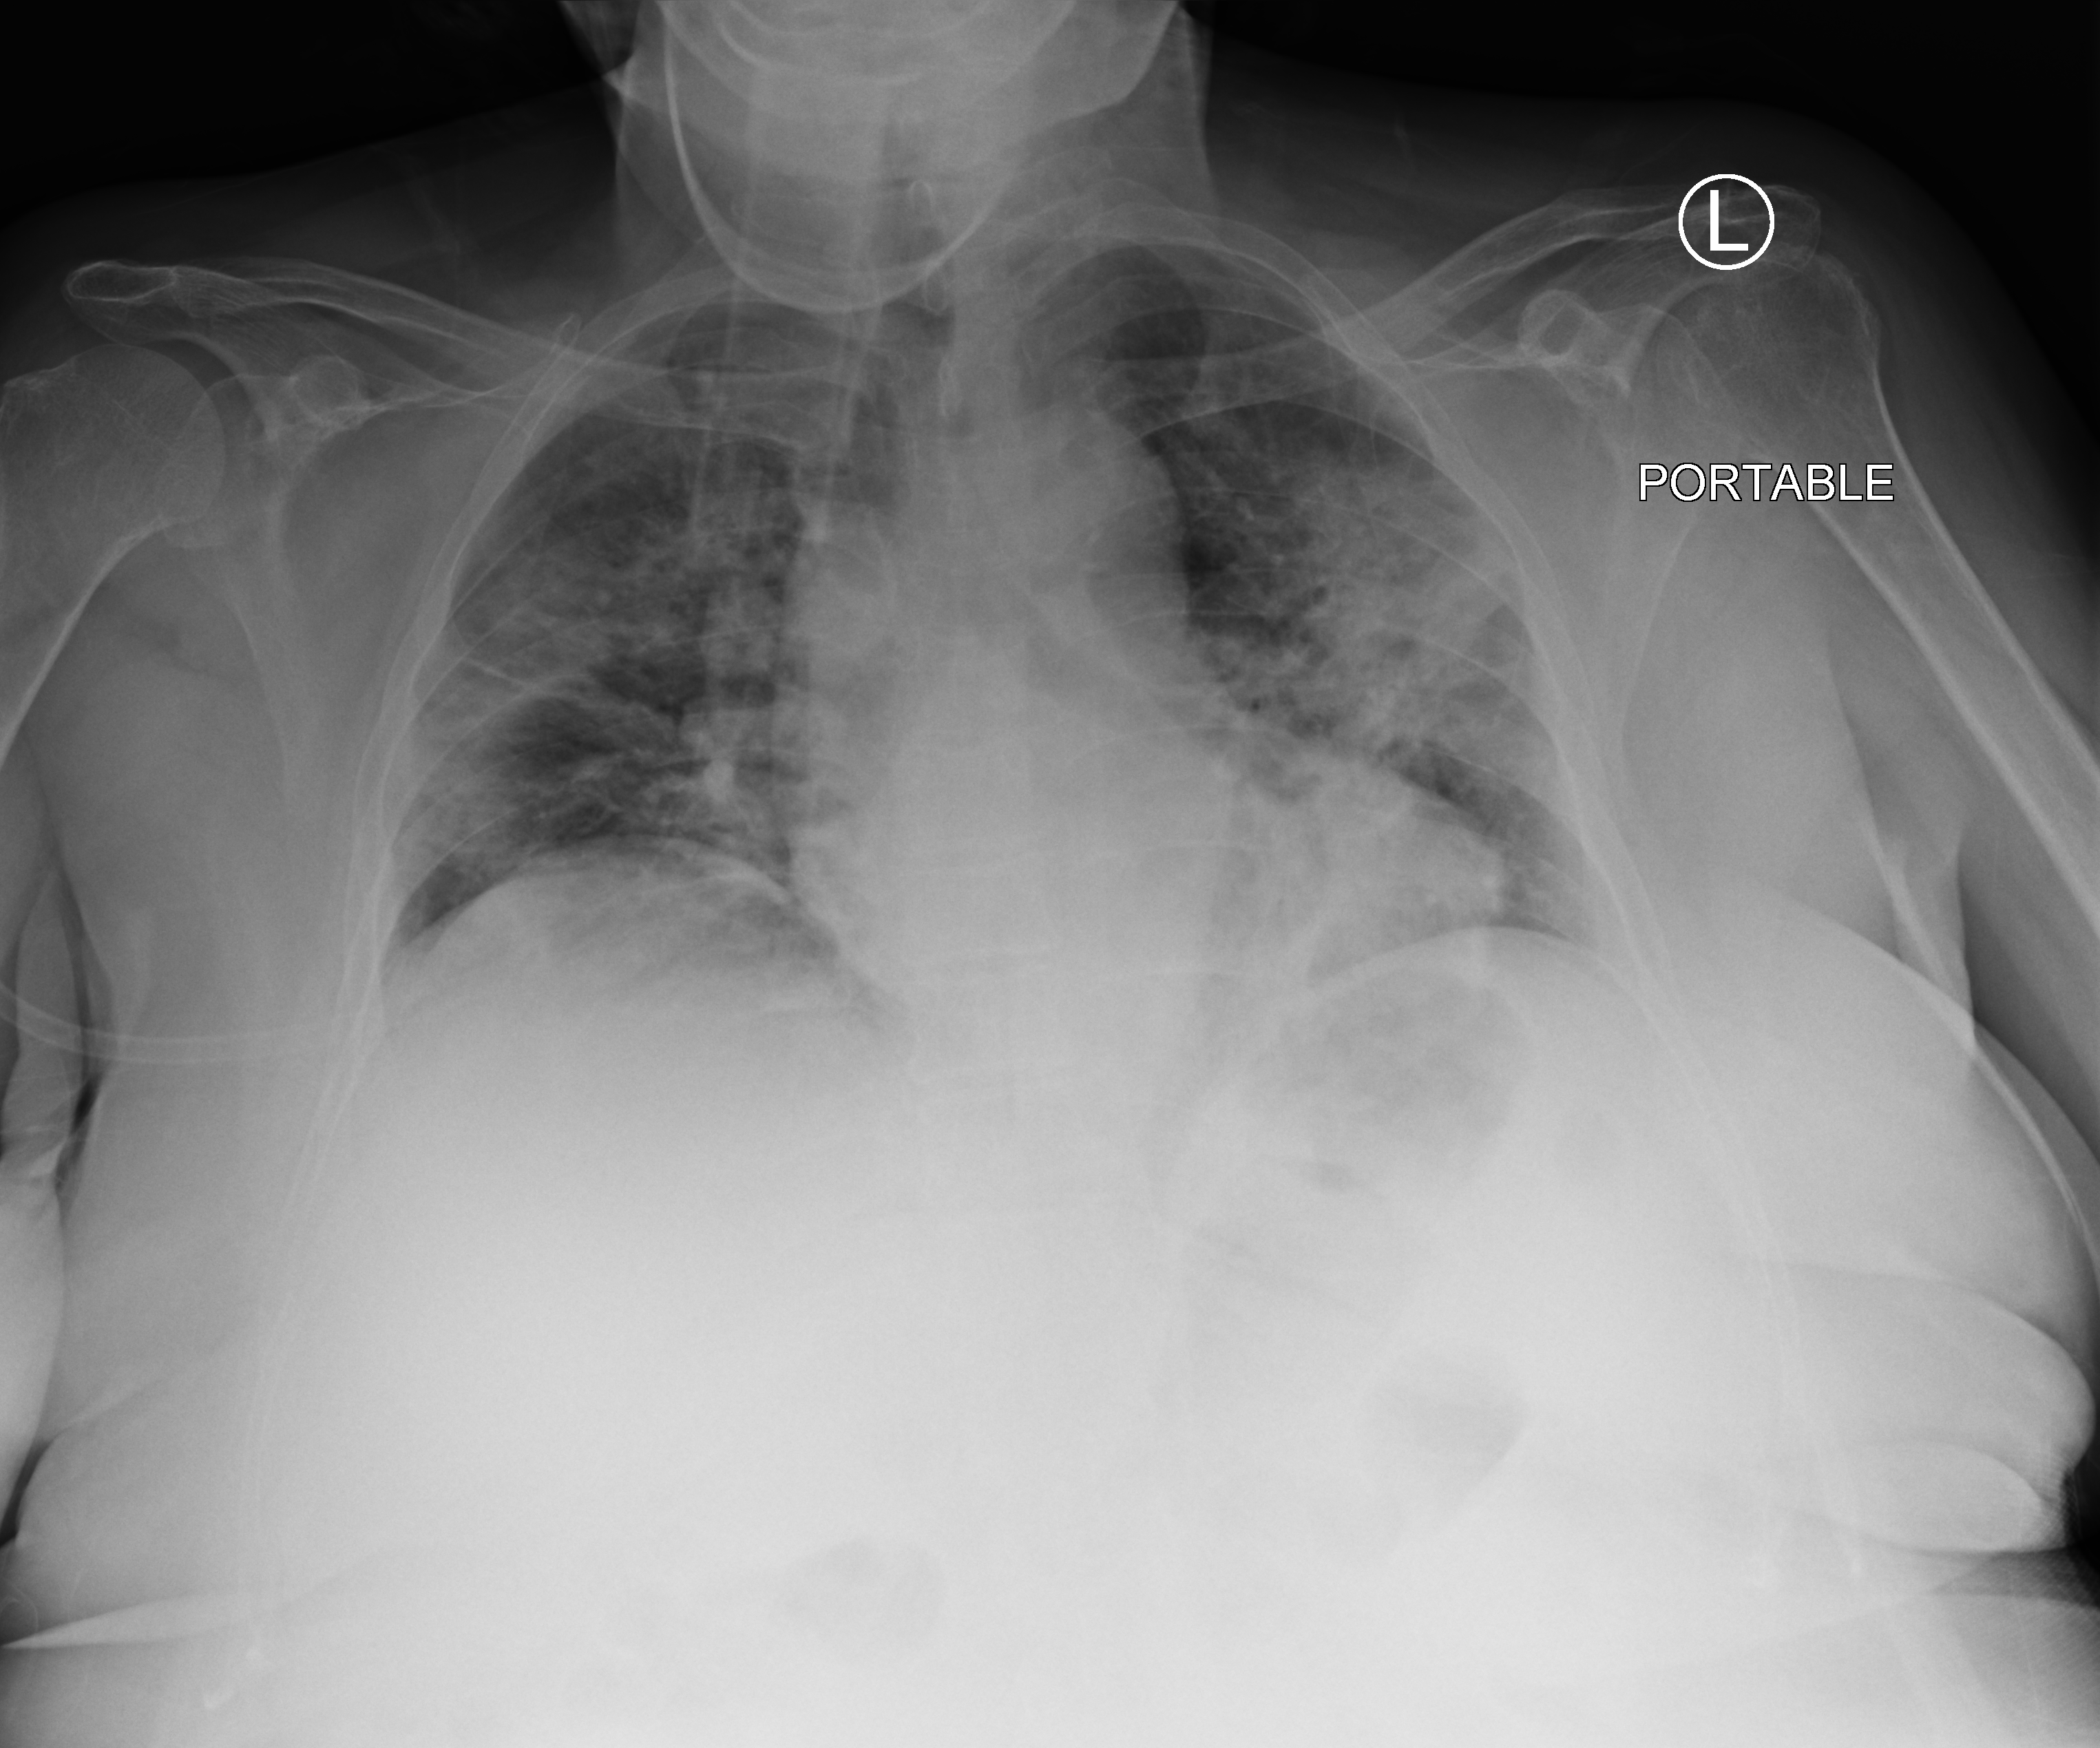
Bedside chest radiograph (computed radiography); anteroposterior (AP) projection. Patient hospitalised with COVID-19; female, aged 60–74 years.
Admission-level facts for this patient (not findings on this image; timing relative to this image not recorded): admitted to intensive care during this hospital stay: yes; mechanically ventilated during this hospital stay: no; hypertension (admission record): yes.